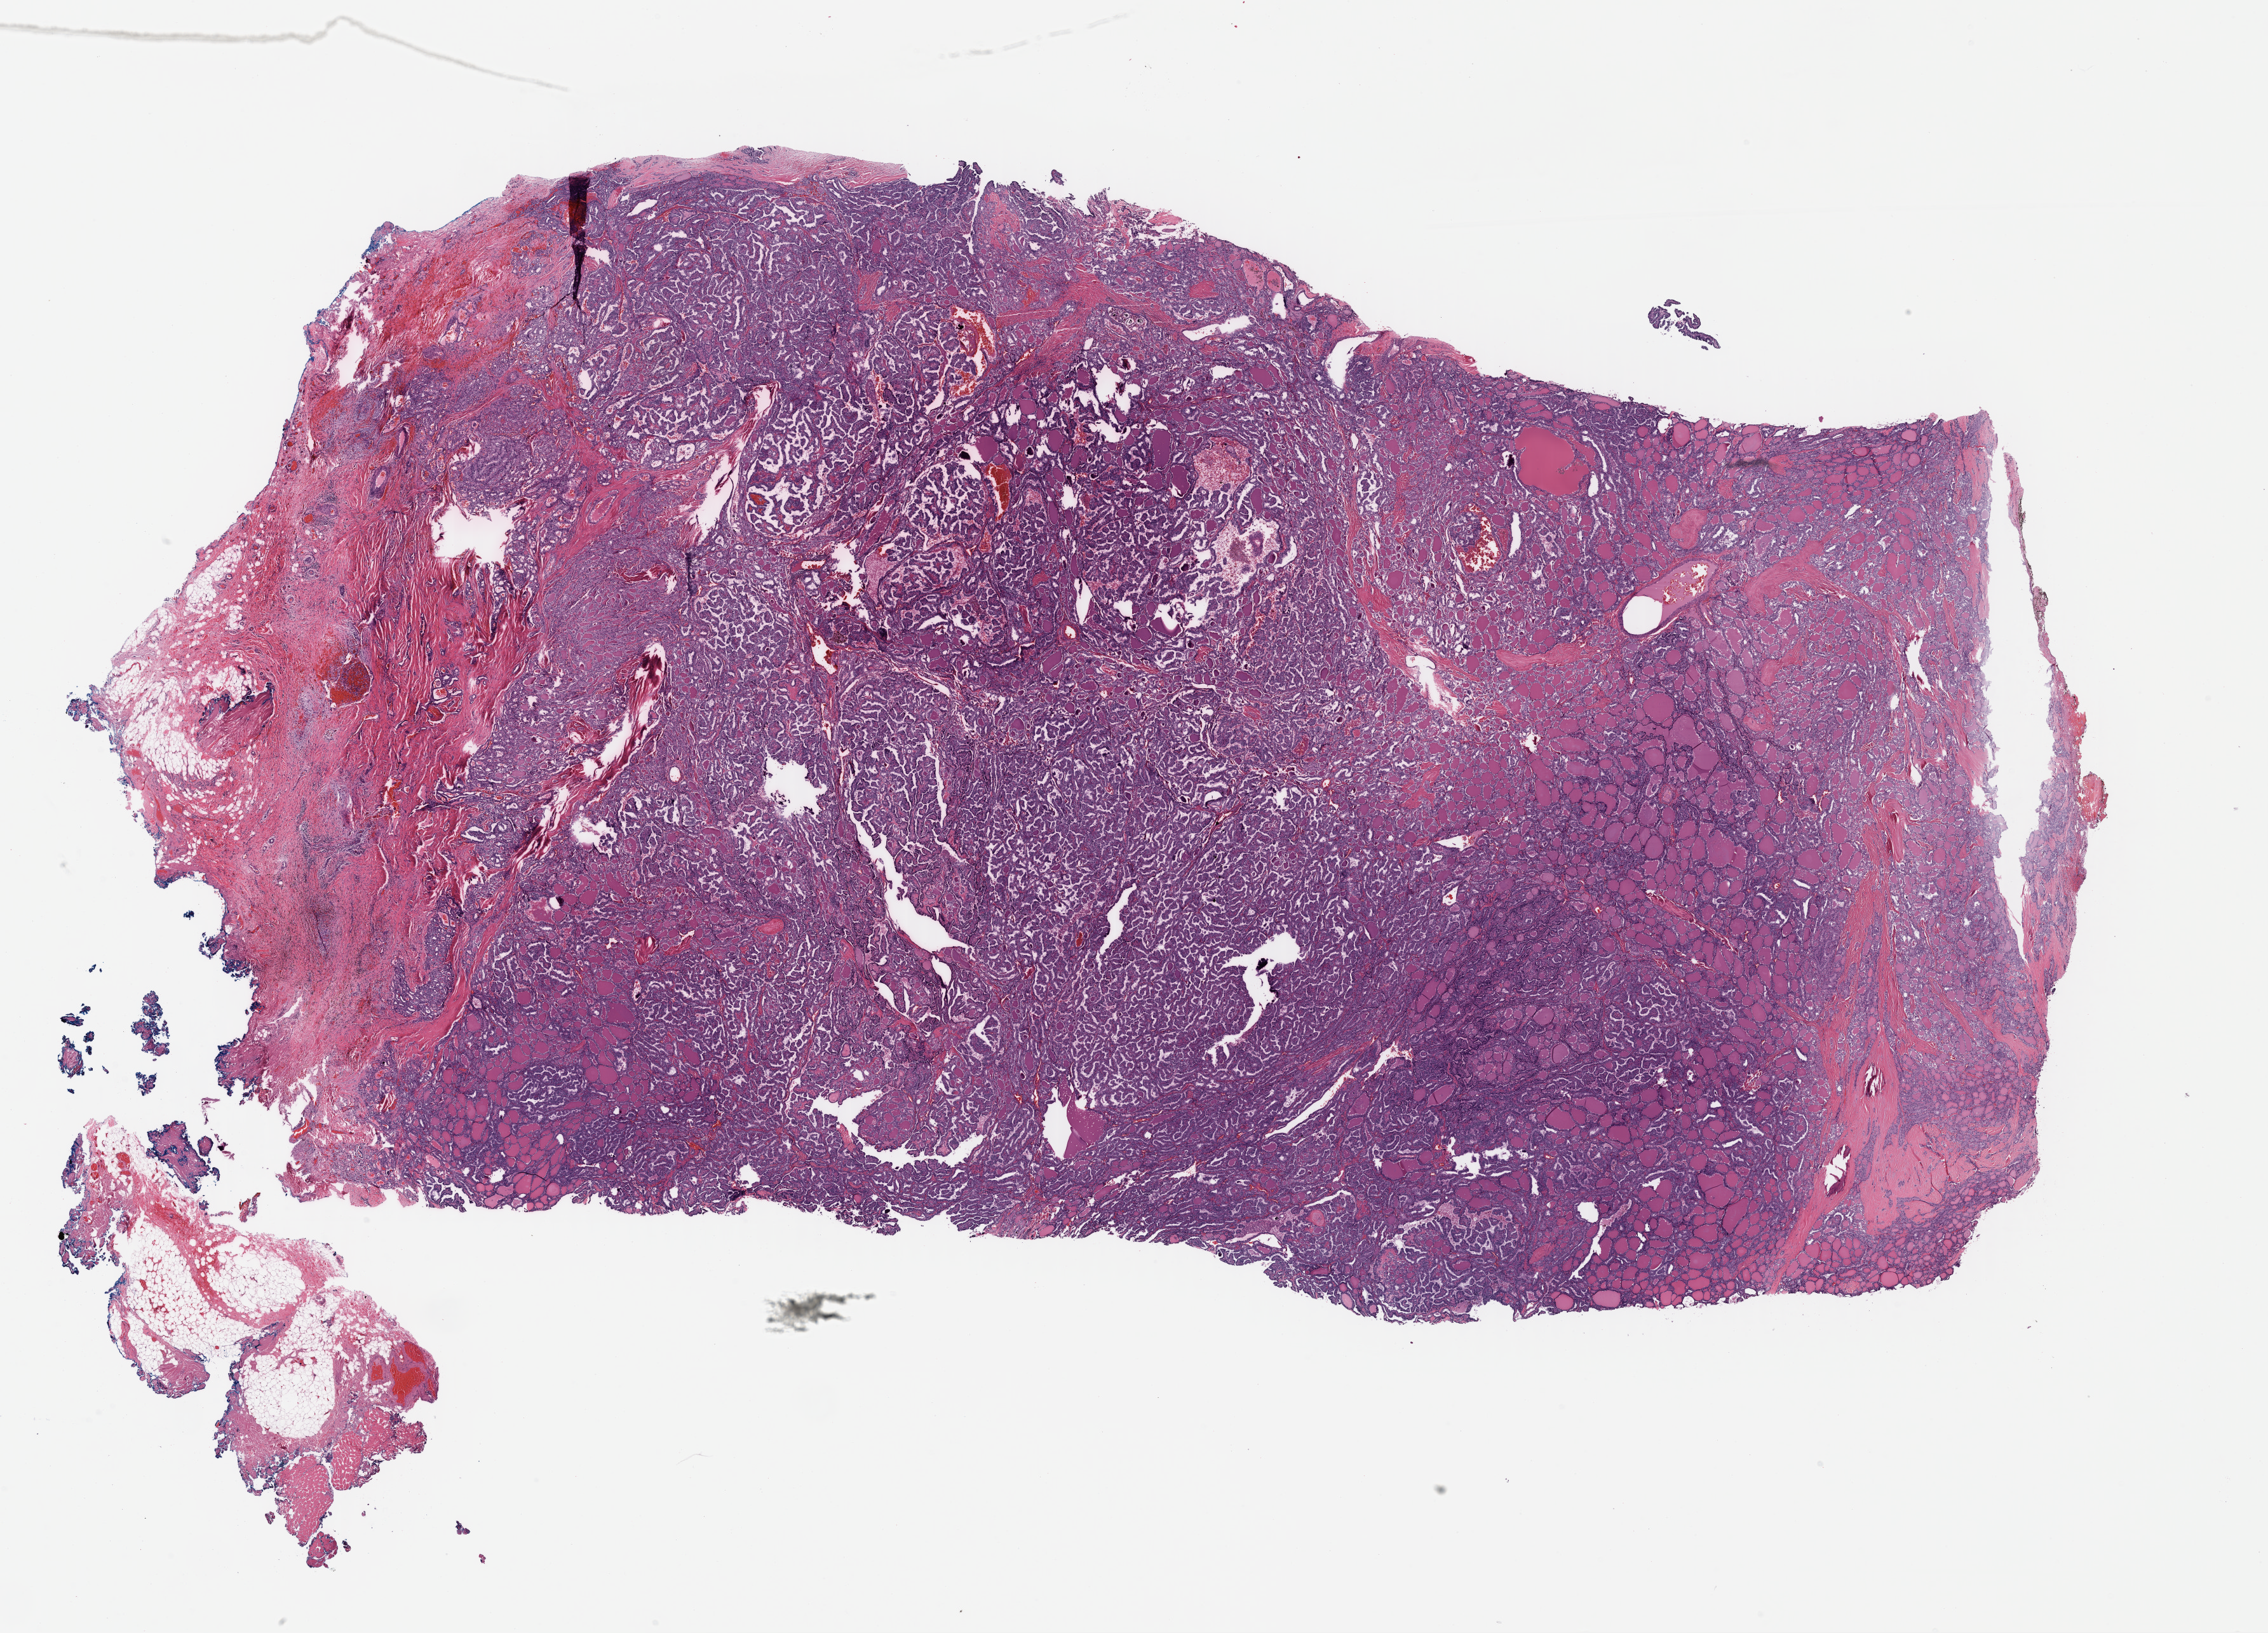
H&E-stained whole-slide image — shown as a low-resolution overview of the whole scanned area (about 28.1 x 20.2 mm, acquisition: 40x scan); formalin-fixed paraffin-embedded (FFPE) diagnostic section; thyroid, primary tumour sample. Female patient; age at initial diagnosis 41 years.
Diagnosis: Papillary adenocarcinoma, NOS (thyroid gland).